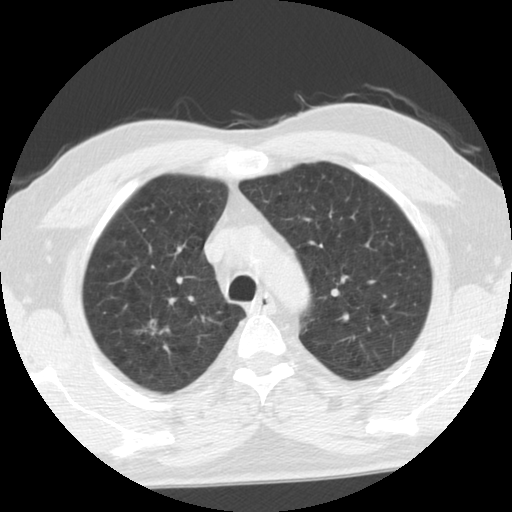
Low-dose screening chest CT, one axial slice. Slice 88 of 116 in the series (ordered by position). Reconstruction kernel STANDARD. Lung window (W 1500 / L -600 HU). 2.5 mm slice thickness. 512 × 512 image matrix, field of view 330 × 330 mm.
Annotated regions visible in this slice (outlined manually by an expert reader):
- lesion 1 (tumor, upper lobe of right lung): bounding box <135,319,172,336> (left, top, right, bottom; pixels)